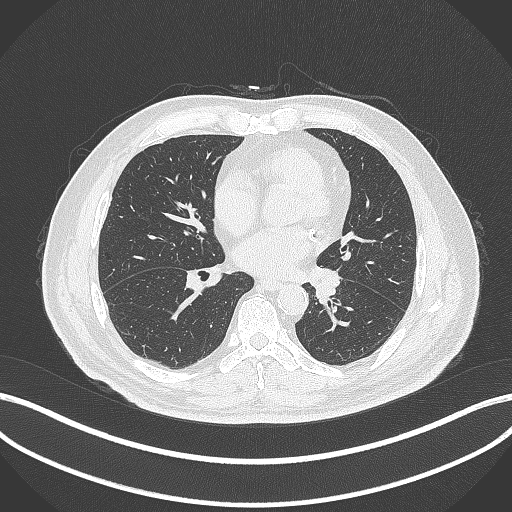
Chest CT, one axial slice. Slice 127 of 312 in the series (ordered by position). Lung window (W 1500 / L -600 HU). 512 × 512 image matrix, field of view 400 × 400 mm. Male patient, age 71 years. From the clinical record (not read from this slice): clinical TNM (as recorded): T1b N0 M0.
Annotated regions visible in this slice (rectangle marked by the reading radiologist):
- lung tumour (recorded histology: squamous cell carcinoma): bounding box (x1, y1, x2, y2) in pixels: (314, 265, 343, 306)